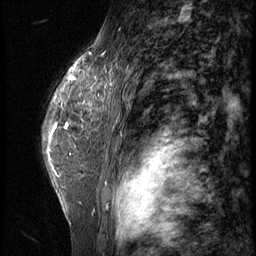
Breast MRI (dynamic contrast-enhanced), one sagittal slice; slice 42 of 62 in the series (ordered by position); 3 images stored at this slice position (order not interpretable as contrast timing); 1.5 T; TE 4.2 ms, TR 9 ms; 256 × 256 image matrix, field of view 180 × 180 mm. Female patient, age 44 years. From the clinical record (not read from this slice): setting: breast cancer imaged before/during neoadjuvant chemotherapy; receptor status: triple-negative.
Annotated regions visible in this slice (semi-automatically segmented with operator editing):
- analysis volume of interest (the breast-tissue region the enhancement analysis was run in; not a lesion): bounding box <77,64,116,125> (left, top, right, bottom; pixels)
- tumour enhancement mask (voxels above the 140 % enhancement threshold inside the analysis volume of interest): <84,70,114,108>